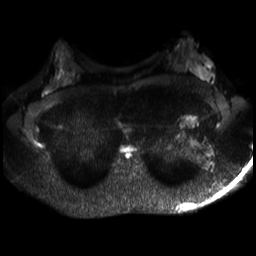
Breast MRI, one axial slice. Position 18 of 30 along the scan axis. Diffusion-weighted series; image 2 of 4 stored at this slice position (different b-values; order by instance number). 3 T. 256 × 256 image matrix, field of view 320 × 320 mm. Female patient.
Outlined on this slice (outlined manually by an expert reader):
- tumour on diffusion-weighted imaging: box from (x=202, y=60) to (x=211, y=79) px